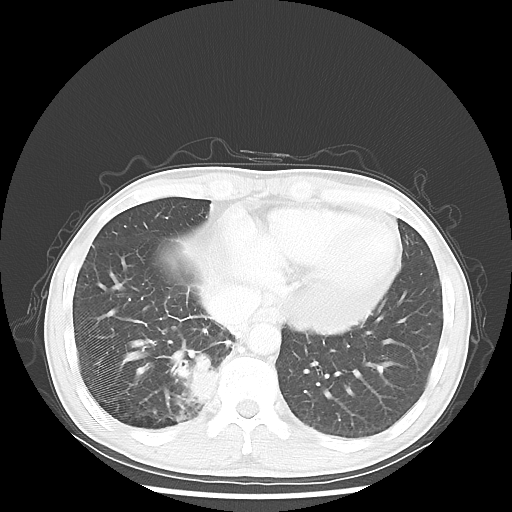
Chest CT, one axial slice. Position 13 of 58 along the scan axis. Lung window (W 1500 / L -600 HU). 512 × 512 image matrix, field of view 360 × 360 mm. Patient: male, 56 years. From the clinical record (not read from this slice): clinical TNM (as recorded): T2 N1 M1; histopathological grade: G1.
Outlined on this slice (rectangle marked by the reading radiologist):
- lung tumour (recorded histology: adenocarcinoma): bounding box <183,349,221,409> (left, top, right, bottom; pixels)